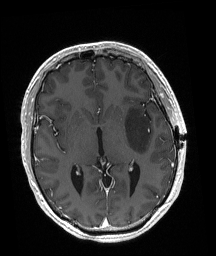
Brain MRI from a brain-tumour surgery series, one axial slice; slice 102 of 192 in the series (ordered by position); T1-weighted post-contrast; 1 mm slice thickness; 216 × 256 image matrix, field of view 211 × 250 mm. Case-level facts recorded for this patient, not image findings: histopathology: Astrocytoma; WHO grade: 3; IDH mutation: yes; tumour location: Left Posterior Frontal.
Annotated regions visible in this slice (expert manual segmentation):
- tumour: bounding box (x1, y1, x2, y2) in pixels: (124, 108, 152, 154)